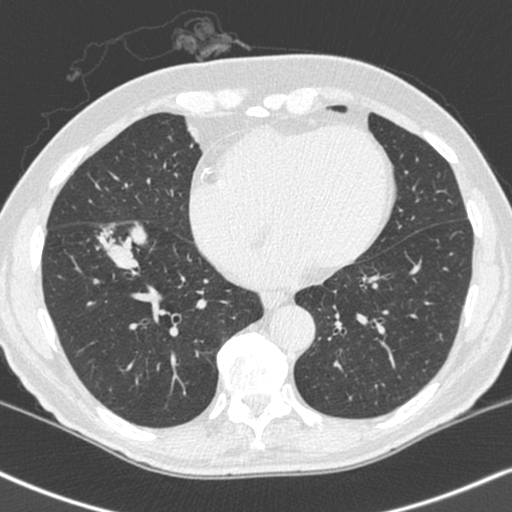
Axial slice from a low-dose chest CT screening exam, baseline screening round, lung window (W 1500 / L -600 HU), 1.3 mm slice thickness, slice 148 of 248 in the series, 512 × 512 image matrix. Male, age 68 years at enrolment. Current smoker at enrolment.
• Lesion marked by an expert reader, bounding box [x1, y1, x2, y2] px = [85, 218, 160, 288].
• The exam's reader record, not a measurement of the box and not confirmed to be the same lesion: non-calcified nodule or mass ≥4 mm, right lower lobe, 34 × 17 mm, smooth margins, soft tissue attenuation.
• Official screen result: positive, change unspecified: nodule(s) >= 4 mm or enlarging nodule(s), mass(es), or other non-specific abnormalities suspicious for lung cancer.
• Later outcome: lung cancer diagnosed 24 days after this screen — combined small cell carcinoma, right lower lobe, stage IIIA (AJCC 6th edition), 41 mm at pathology.